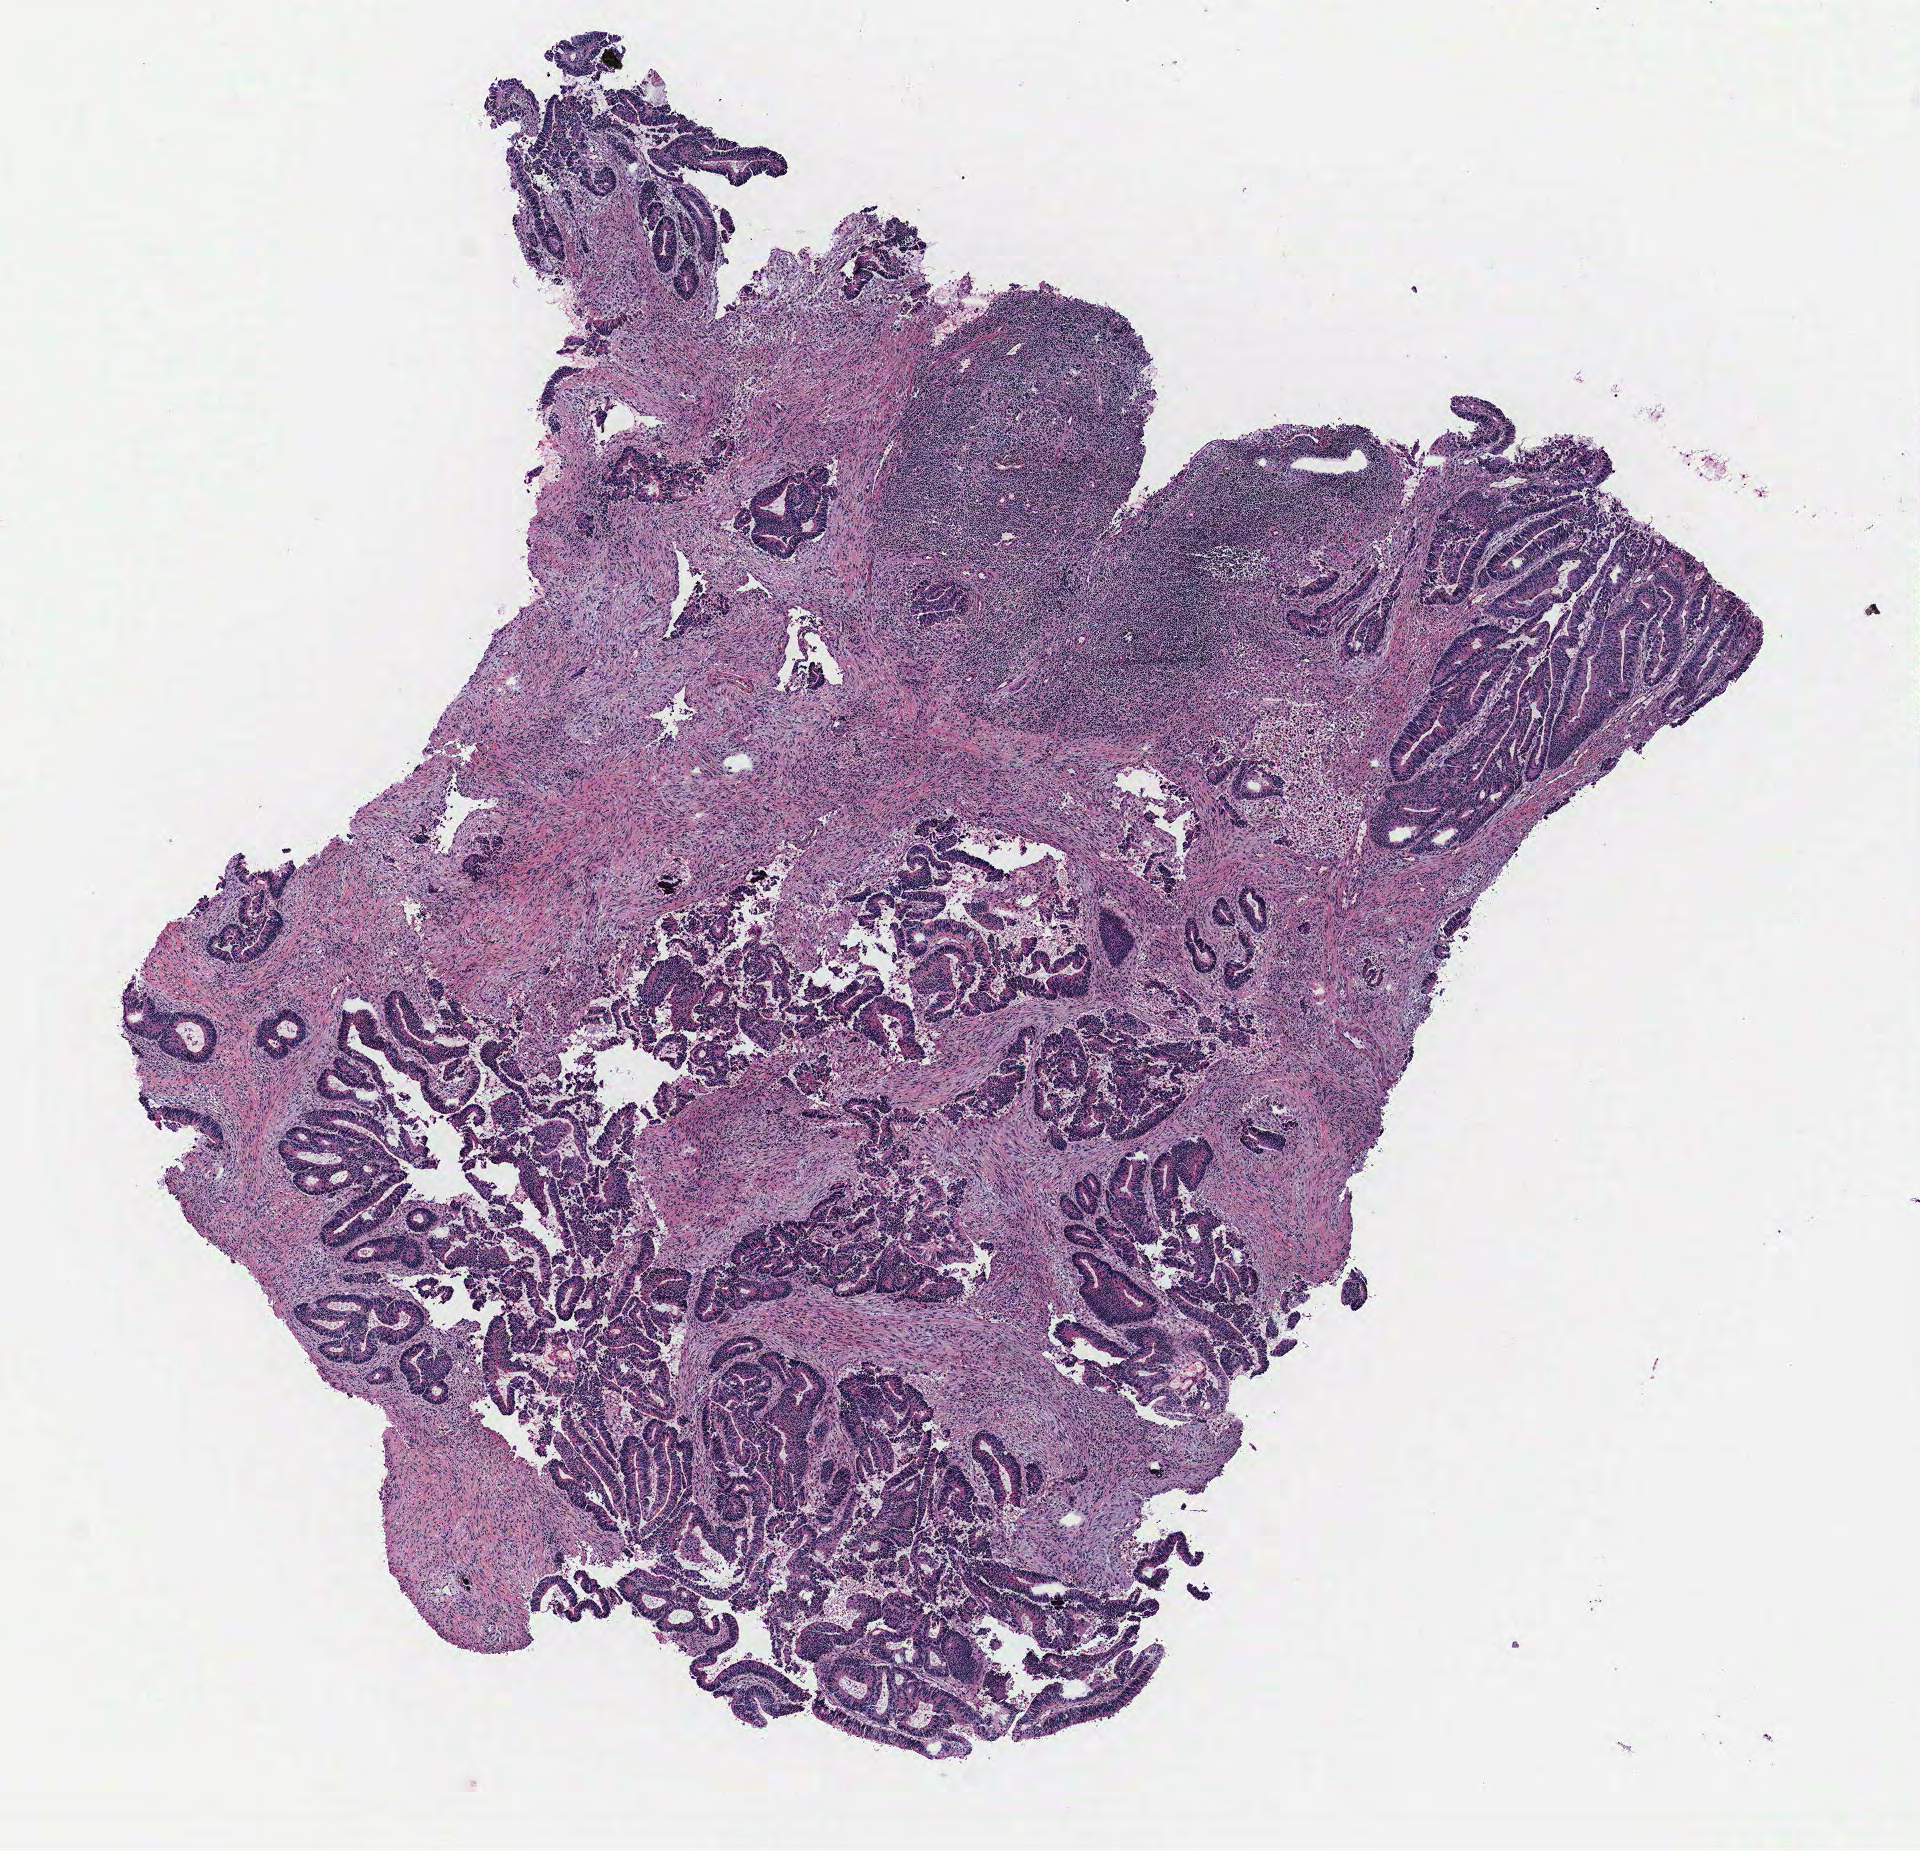
H&E-stained whole-slide image, shown as a low-resolution overview of the whole scanned area (about 7.7 x 7.4 mm, from a 40x scan), colon, tissue type not recorded.
Patient diagnosis (cohort enrolment): colon cancer (colon).